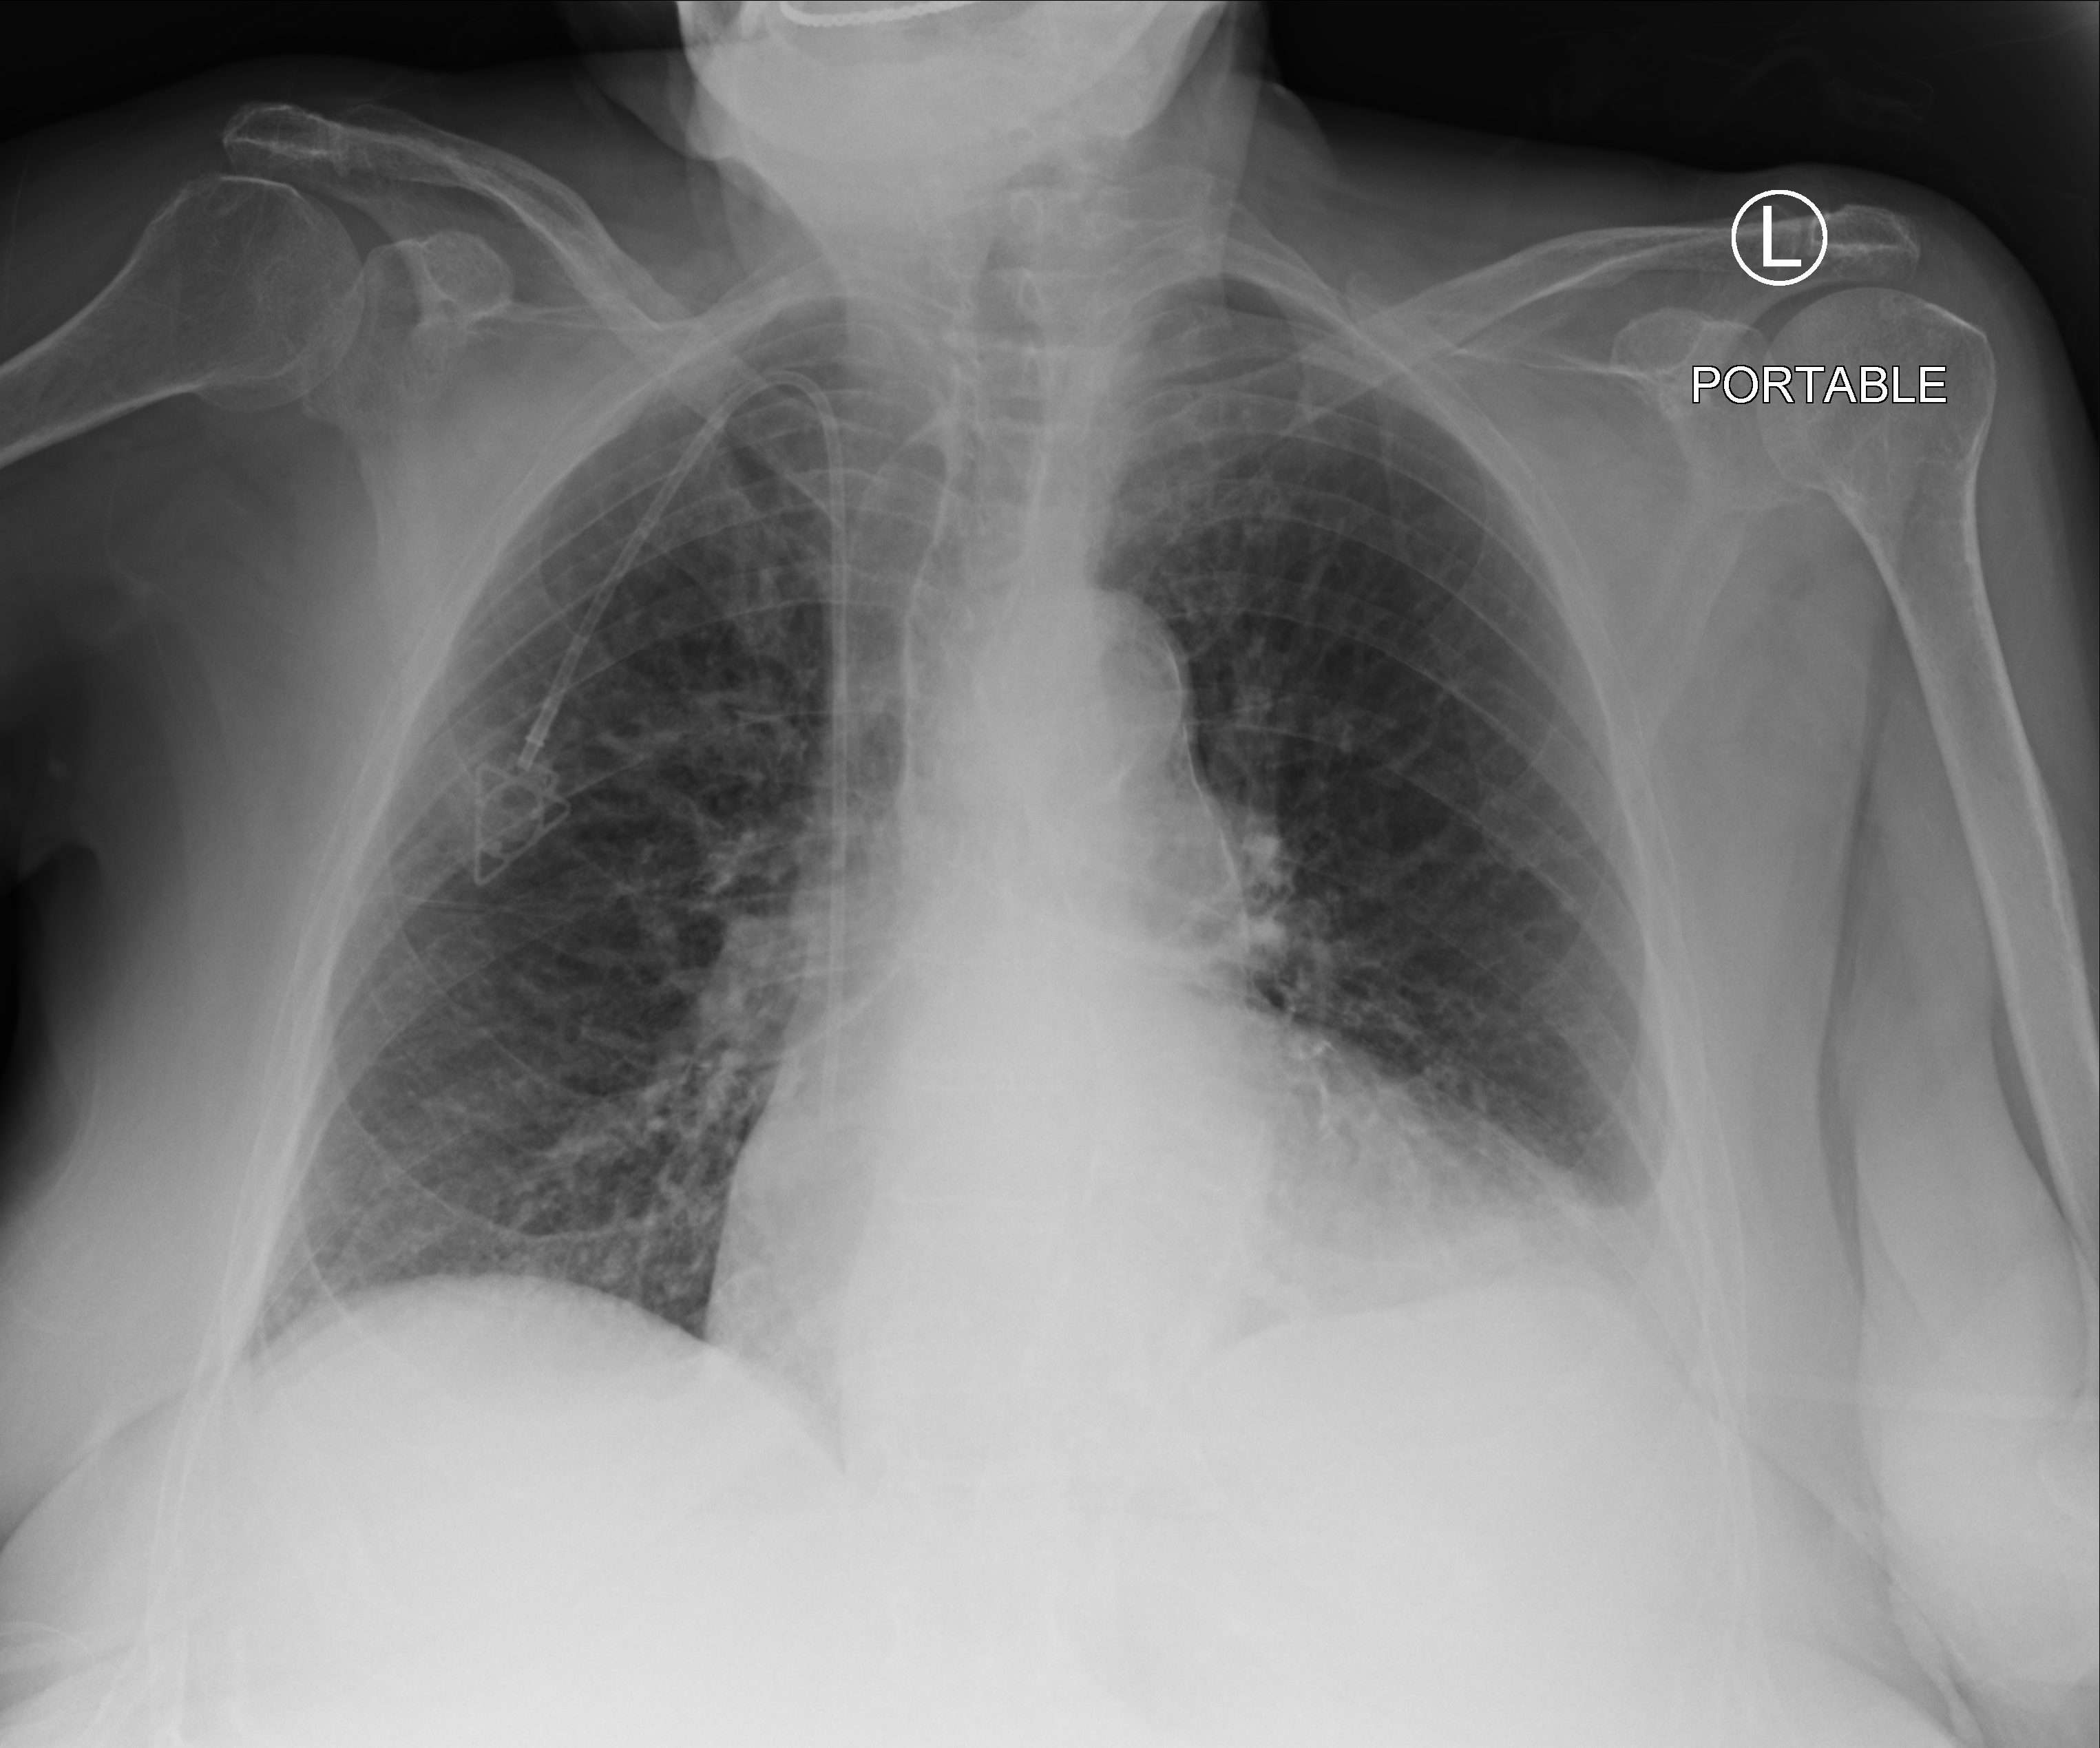
Portable chest radiograph, anteroposterior (AP) projection. Patient hospitalised with COVID-19; female, aged 75–90 years.
Hospital-stay facts (about this admission, not read from this image; timing relative to this image not recorded):
- mechanically ventilated during this hospital stay: no
- admitted to intensive care during this hospital stay: no